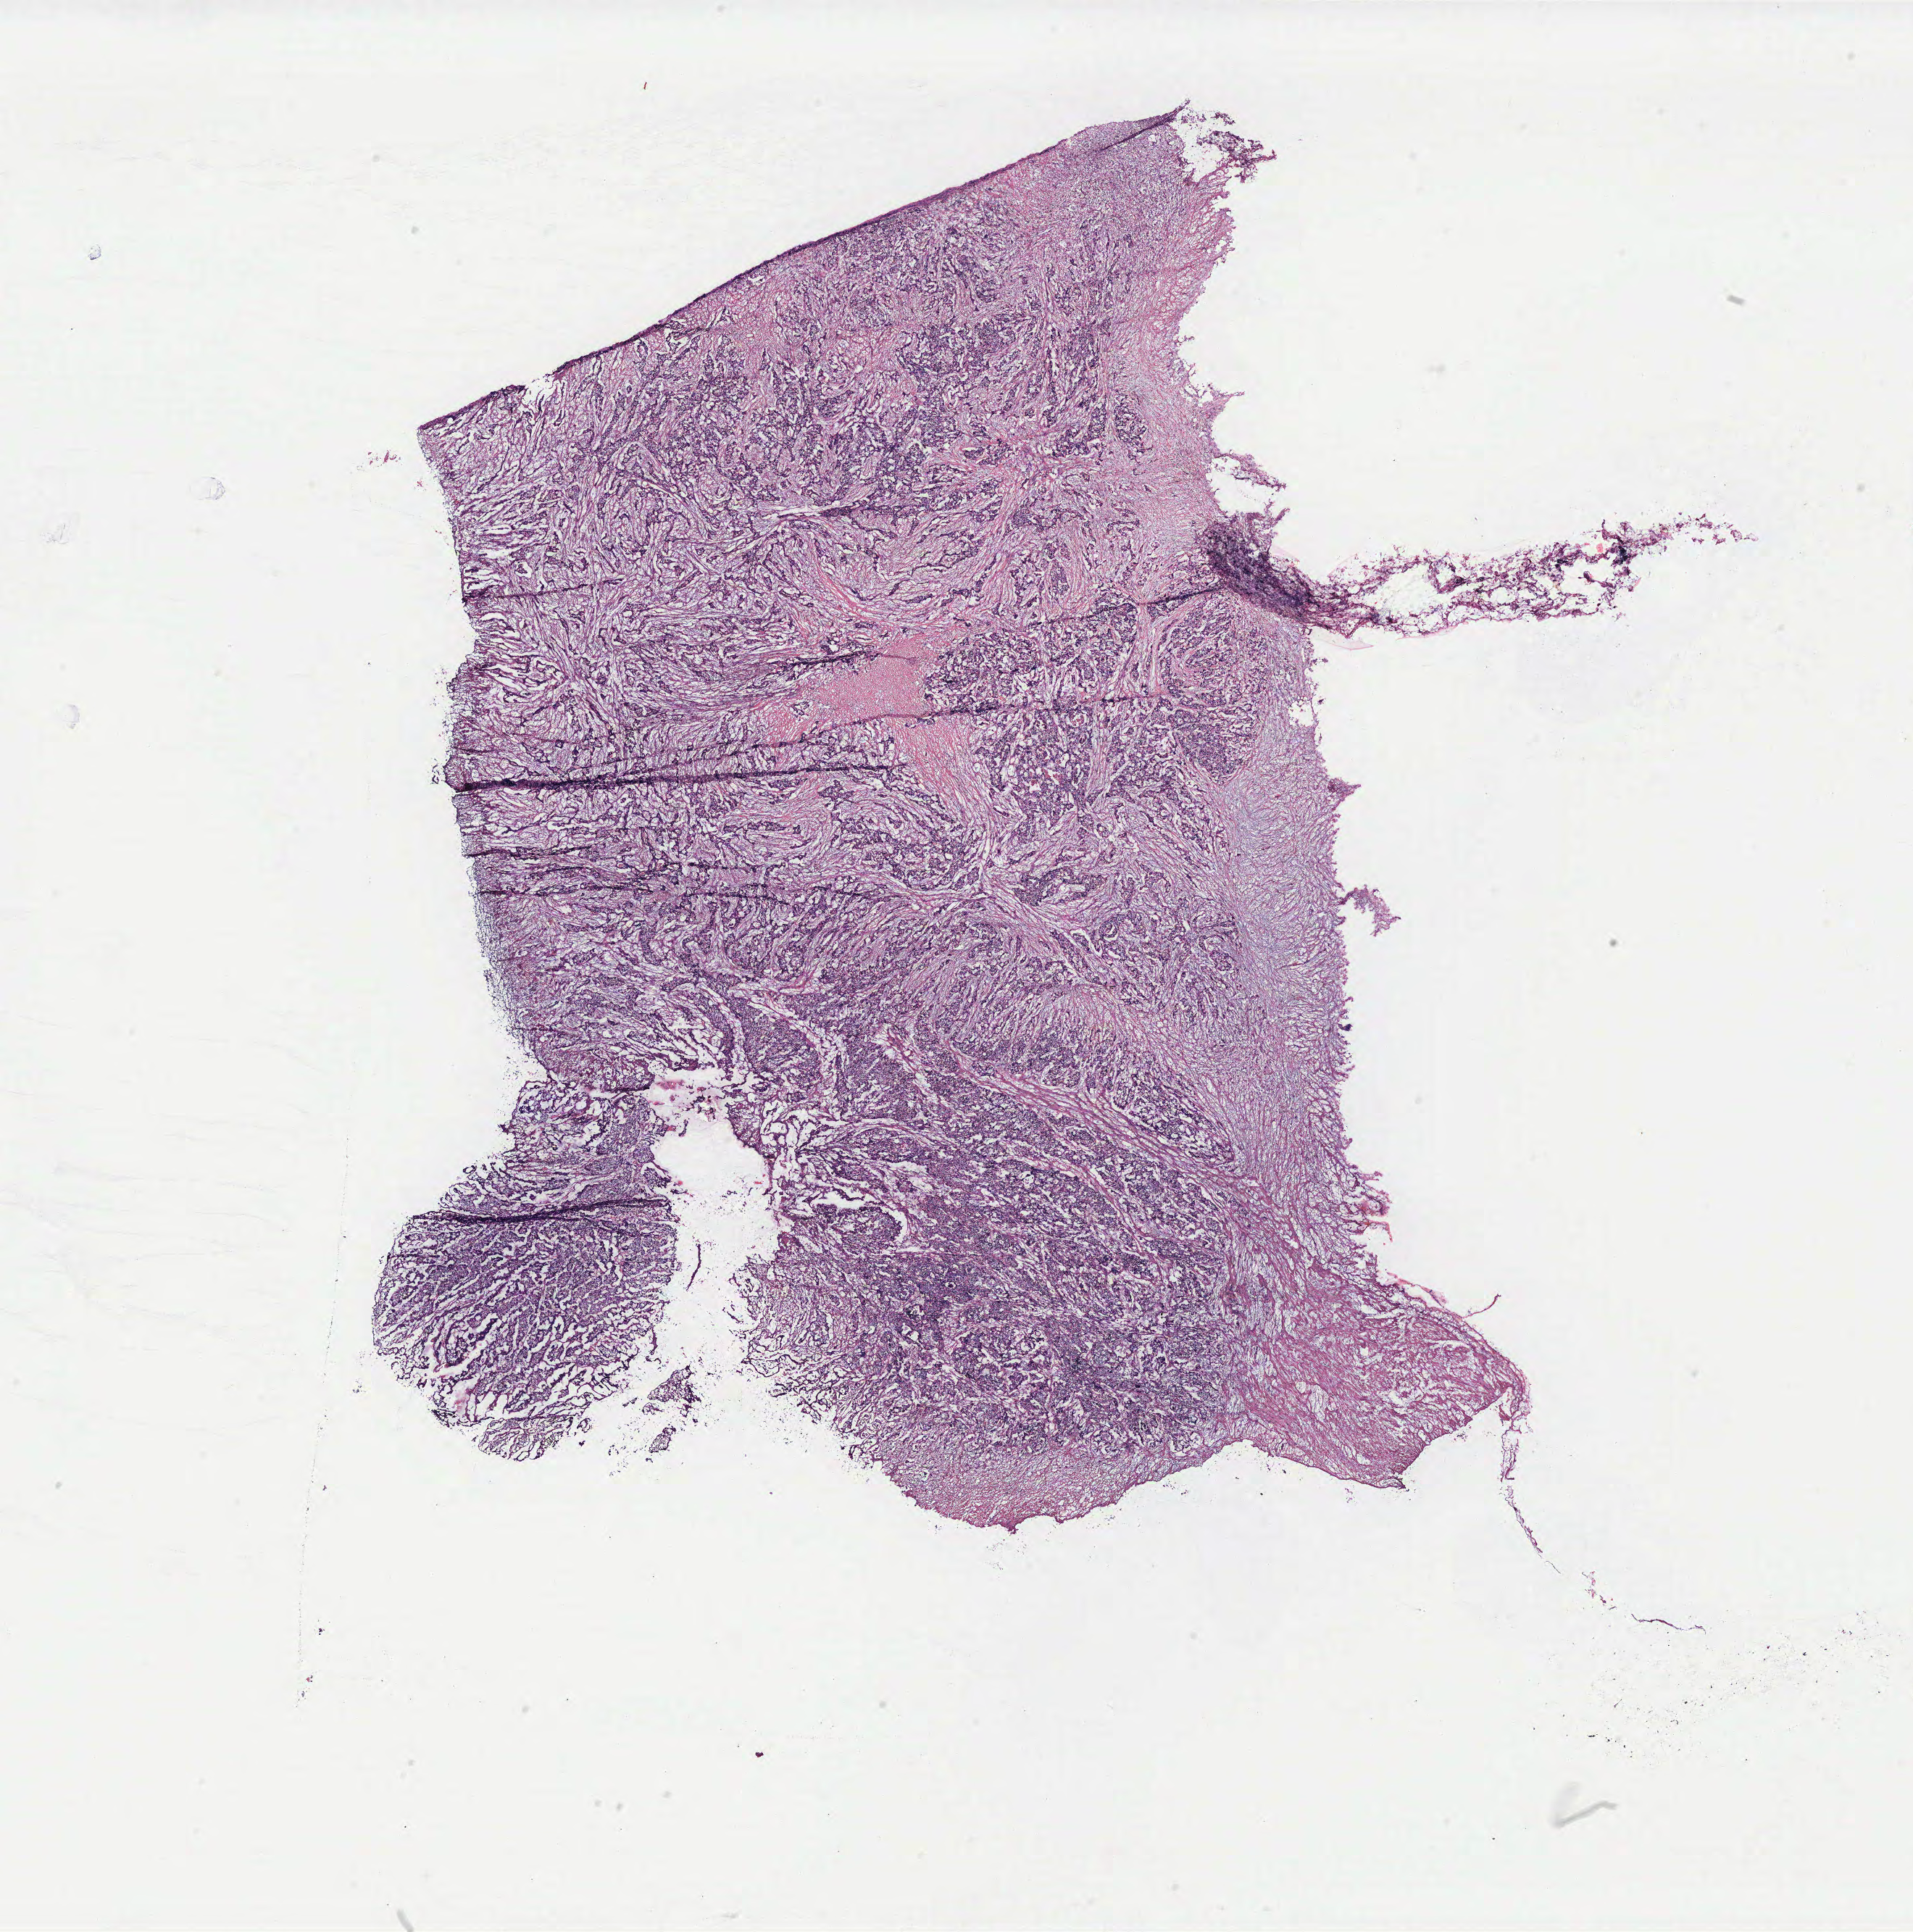
Whole-slide histology image, Hematoxylin and eosin (H&E) stained — a low-resolution overview of the entire scanned area, about 21.1 x 21.3 mm, colon, normal (non-tumour) tissue. Patient: female, age 67 years.
- this section: normal (non-tumour) tissue from the same patient
- patient diagnosis: Adenocarcinoma, NOS